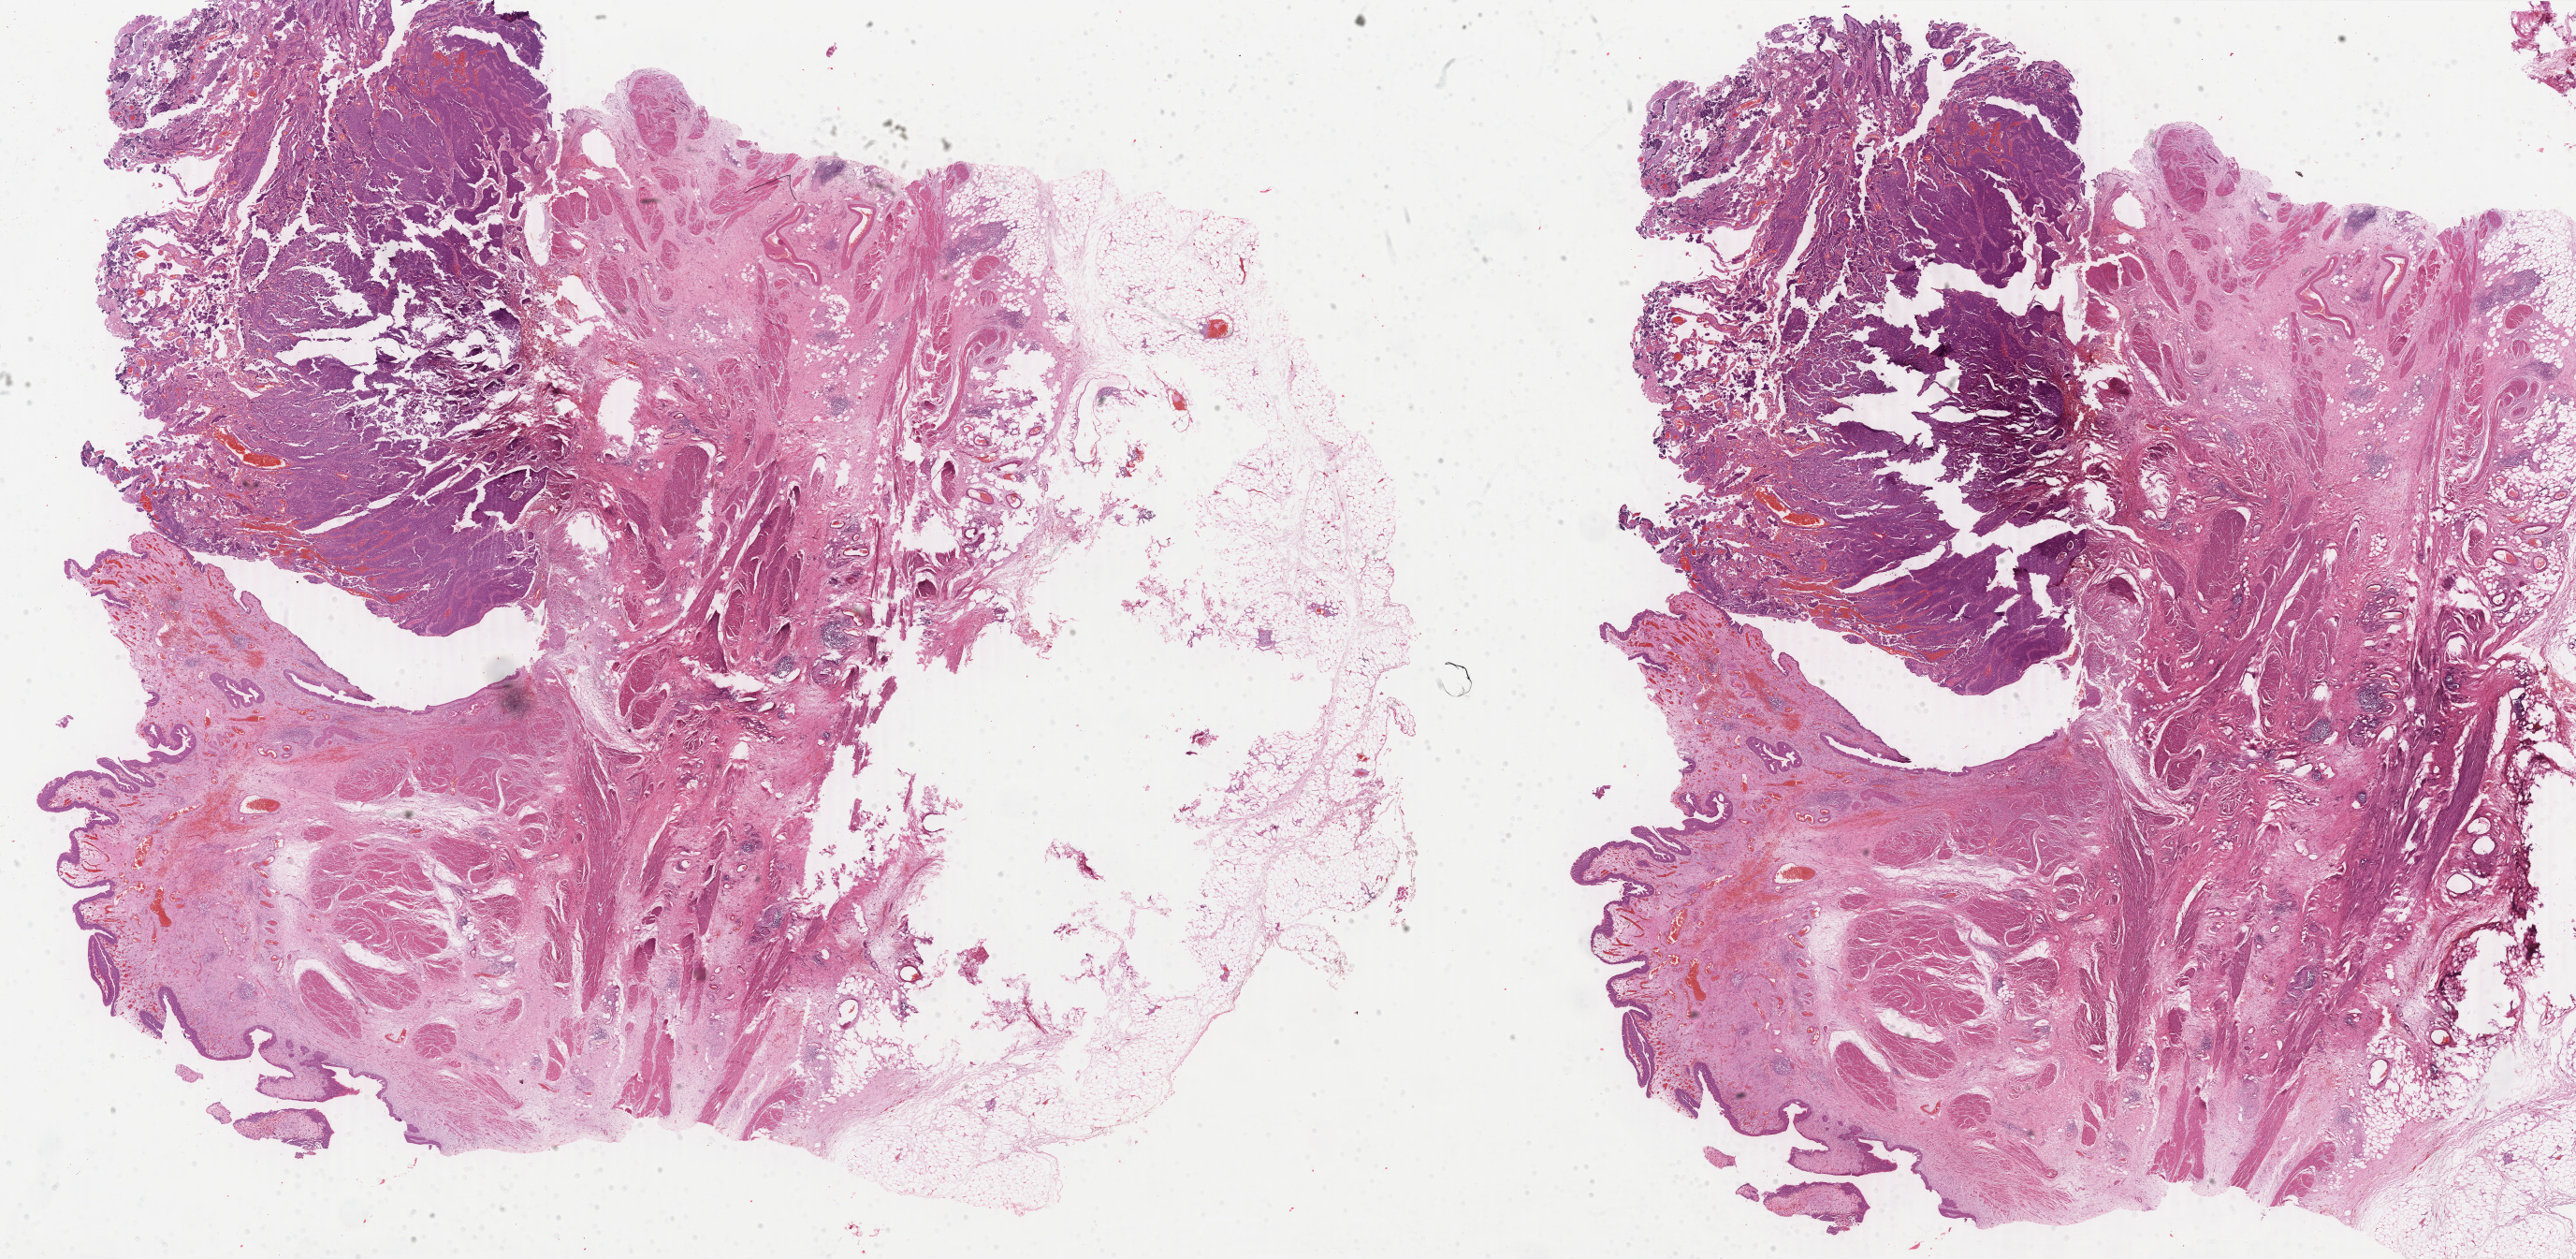
Whole-slide histology image, H&E-stained — whole scanned area (about 43.8 x 21.4 mm) shown as a low-resolution overview; FFPE section; primary tumour sample from the bladder. Patient: male, age at initial diagnosis 57 years. Histologic grade: high grade.
* AJCC pathologic stage: II
* pathologic diagnosis: Transitional cell carcinoma (lateral wall of bladder)
* TNM: T2a NX MX